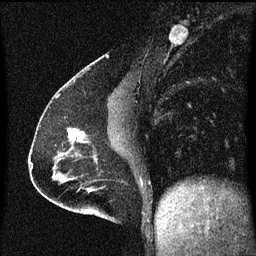
Breast MRI (dynamic contrast-enhanced), one sagittal slice; position 25 of 60 along the scan axis; dynamic contrast-enhanced series, image 2 of 3 at this slice position (ordered by acquisition); 1.5 T; TE 4.2 ms, TR 8 ms; 2 mm slice thickness; 256 × 256 image matrix, field of view 200 × 200 mm. Patient: female, 51 years.
Annotated regions visible in this slice (semi-automatically segmented with operator editing):
- analysis volume of interest (the breast-tissue region the enhancement analysis was run in; not a lesion): bounding box (x1, y1, x2, y2) in pixels: (68, 128, 91, 149)
- tumour enhancement mask (voxels above the 70 % enhancement threshold inside the analysis volume of interest): (68, 128, 85, 143)